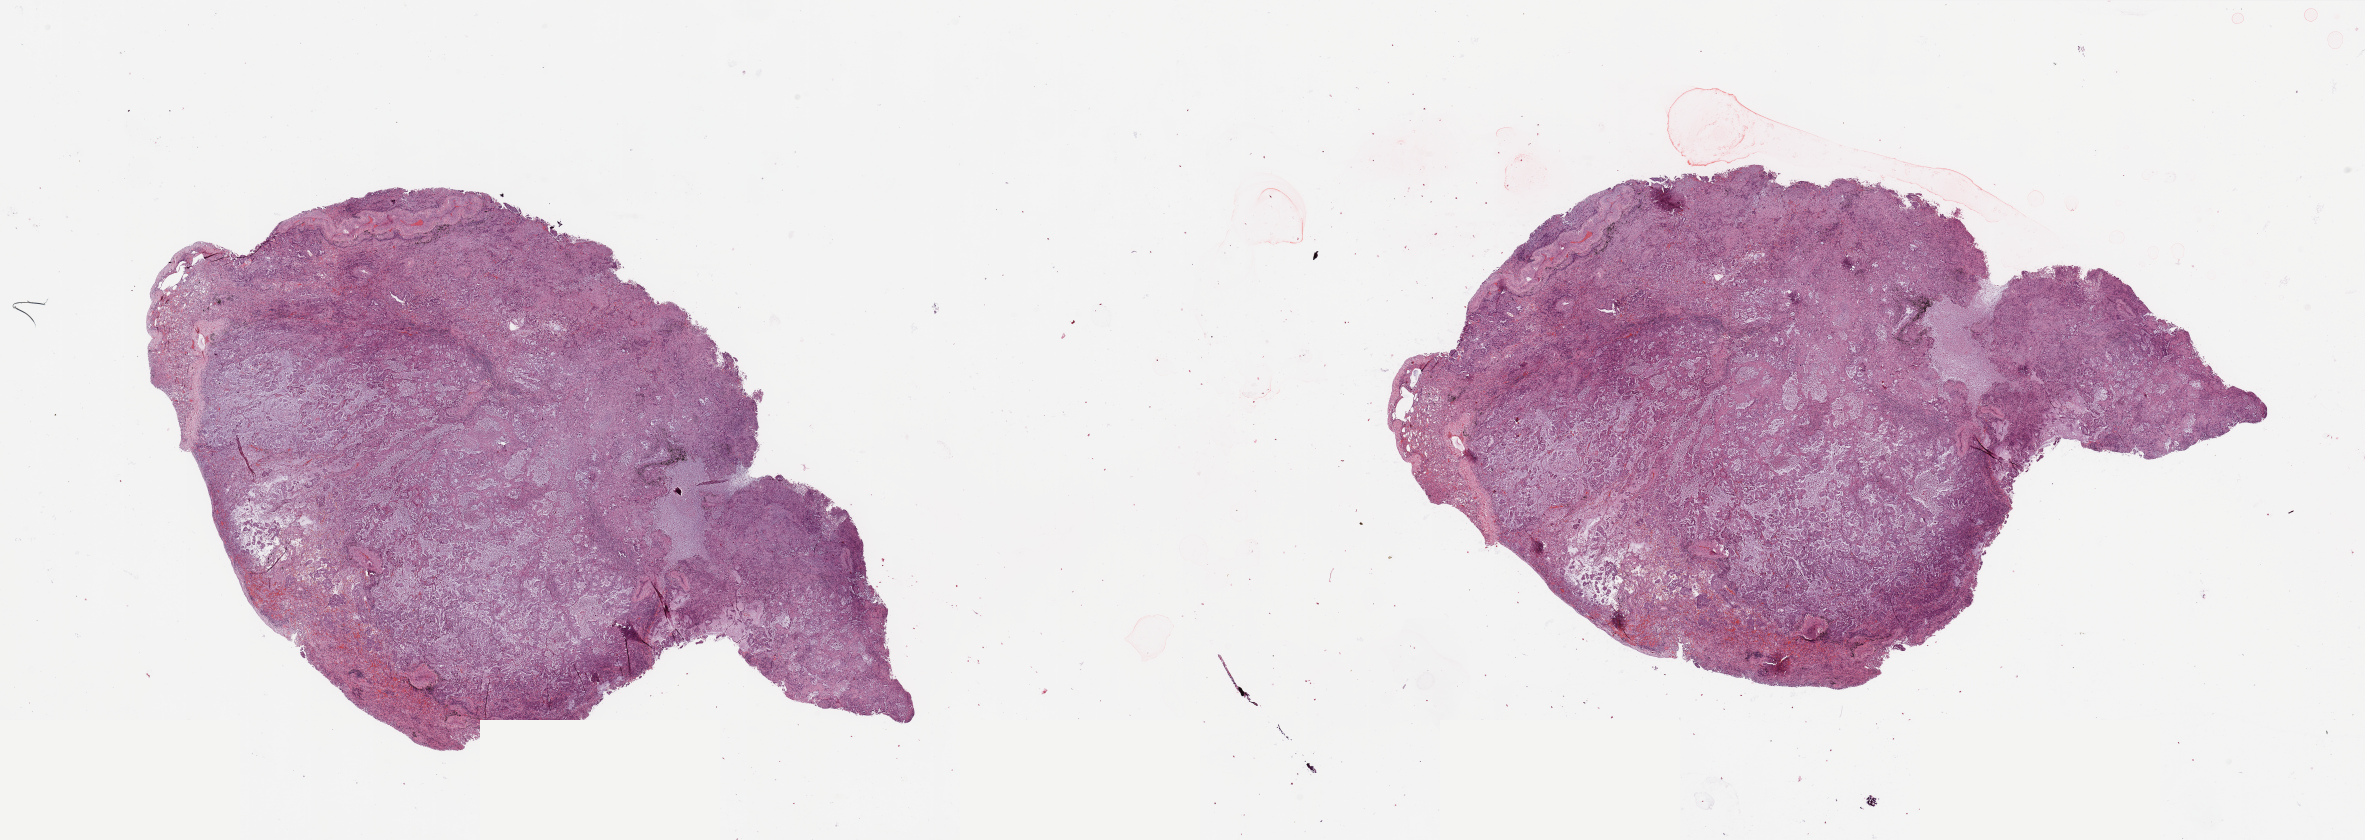
H&E-stained whole-slide image — whole scanned area (about 37.4 x 13.3 mm, from a 20x scan) shown as a low-resolution overview, lung, tumour tissue. Female, 70 y/o. Histologic grade: G1 (well differentiated).
• AJCC pathologic stage: IIIA
• diagnosis: Adenocarcinoma, NOS